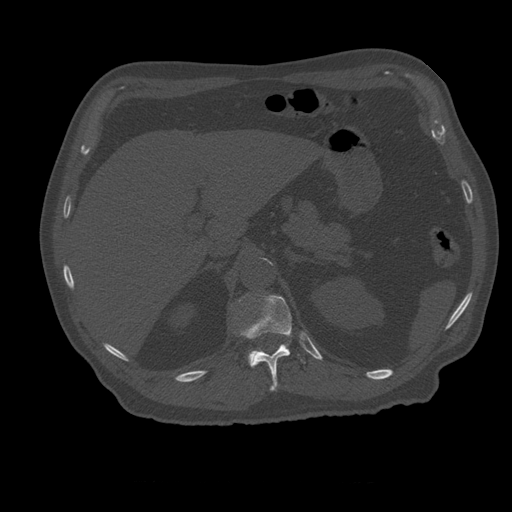
CT including the spine, one axial slice; slice 257 of 399 in the series (ordered by position); reconstruction kernel STANDARD; 120 kVp; bone window (W 1800 / L 400 HU); 512 × 512 image matrix. Patient age 73 years. From the clinical record (not read from this slice): primary cancer: prostate.
Outlined on this slice (semi-automatically segmented with operator editing):
- L1 vertebra: bounding box <239,324,288,366> (left, top, right, bottom; pixels)
- T12 vertebra: <240,295,292,391>